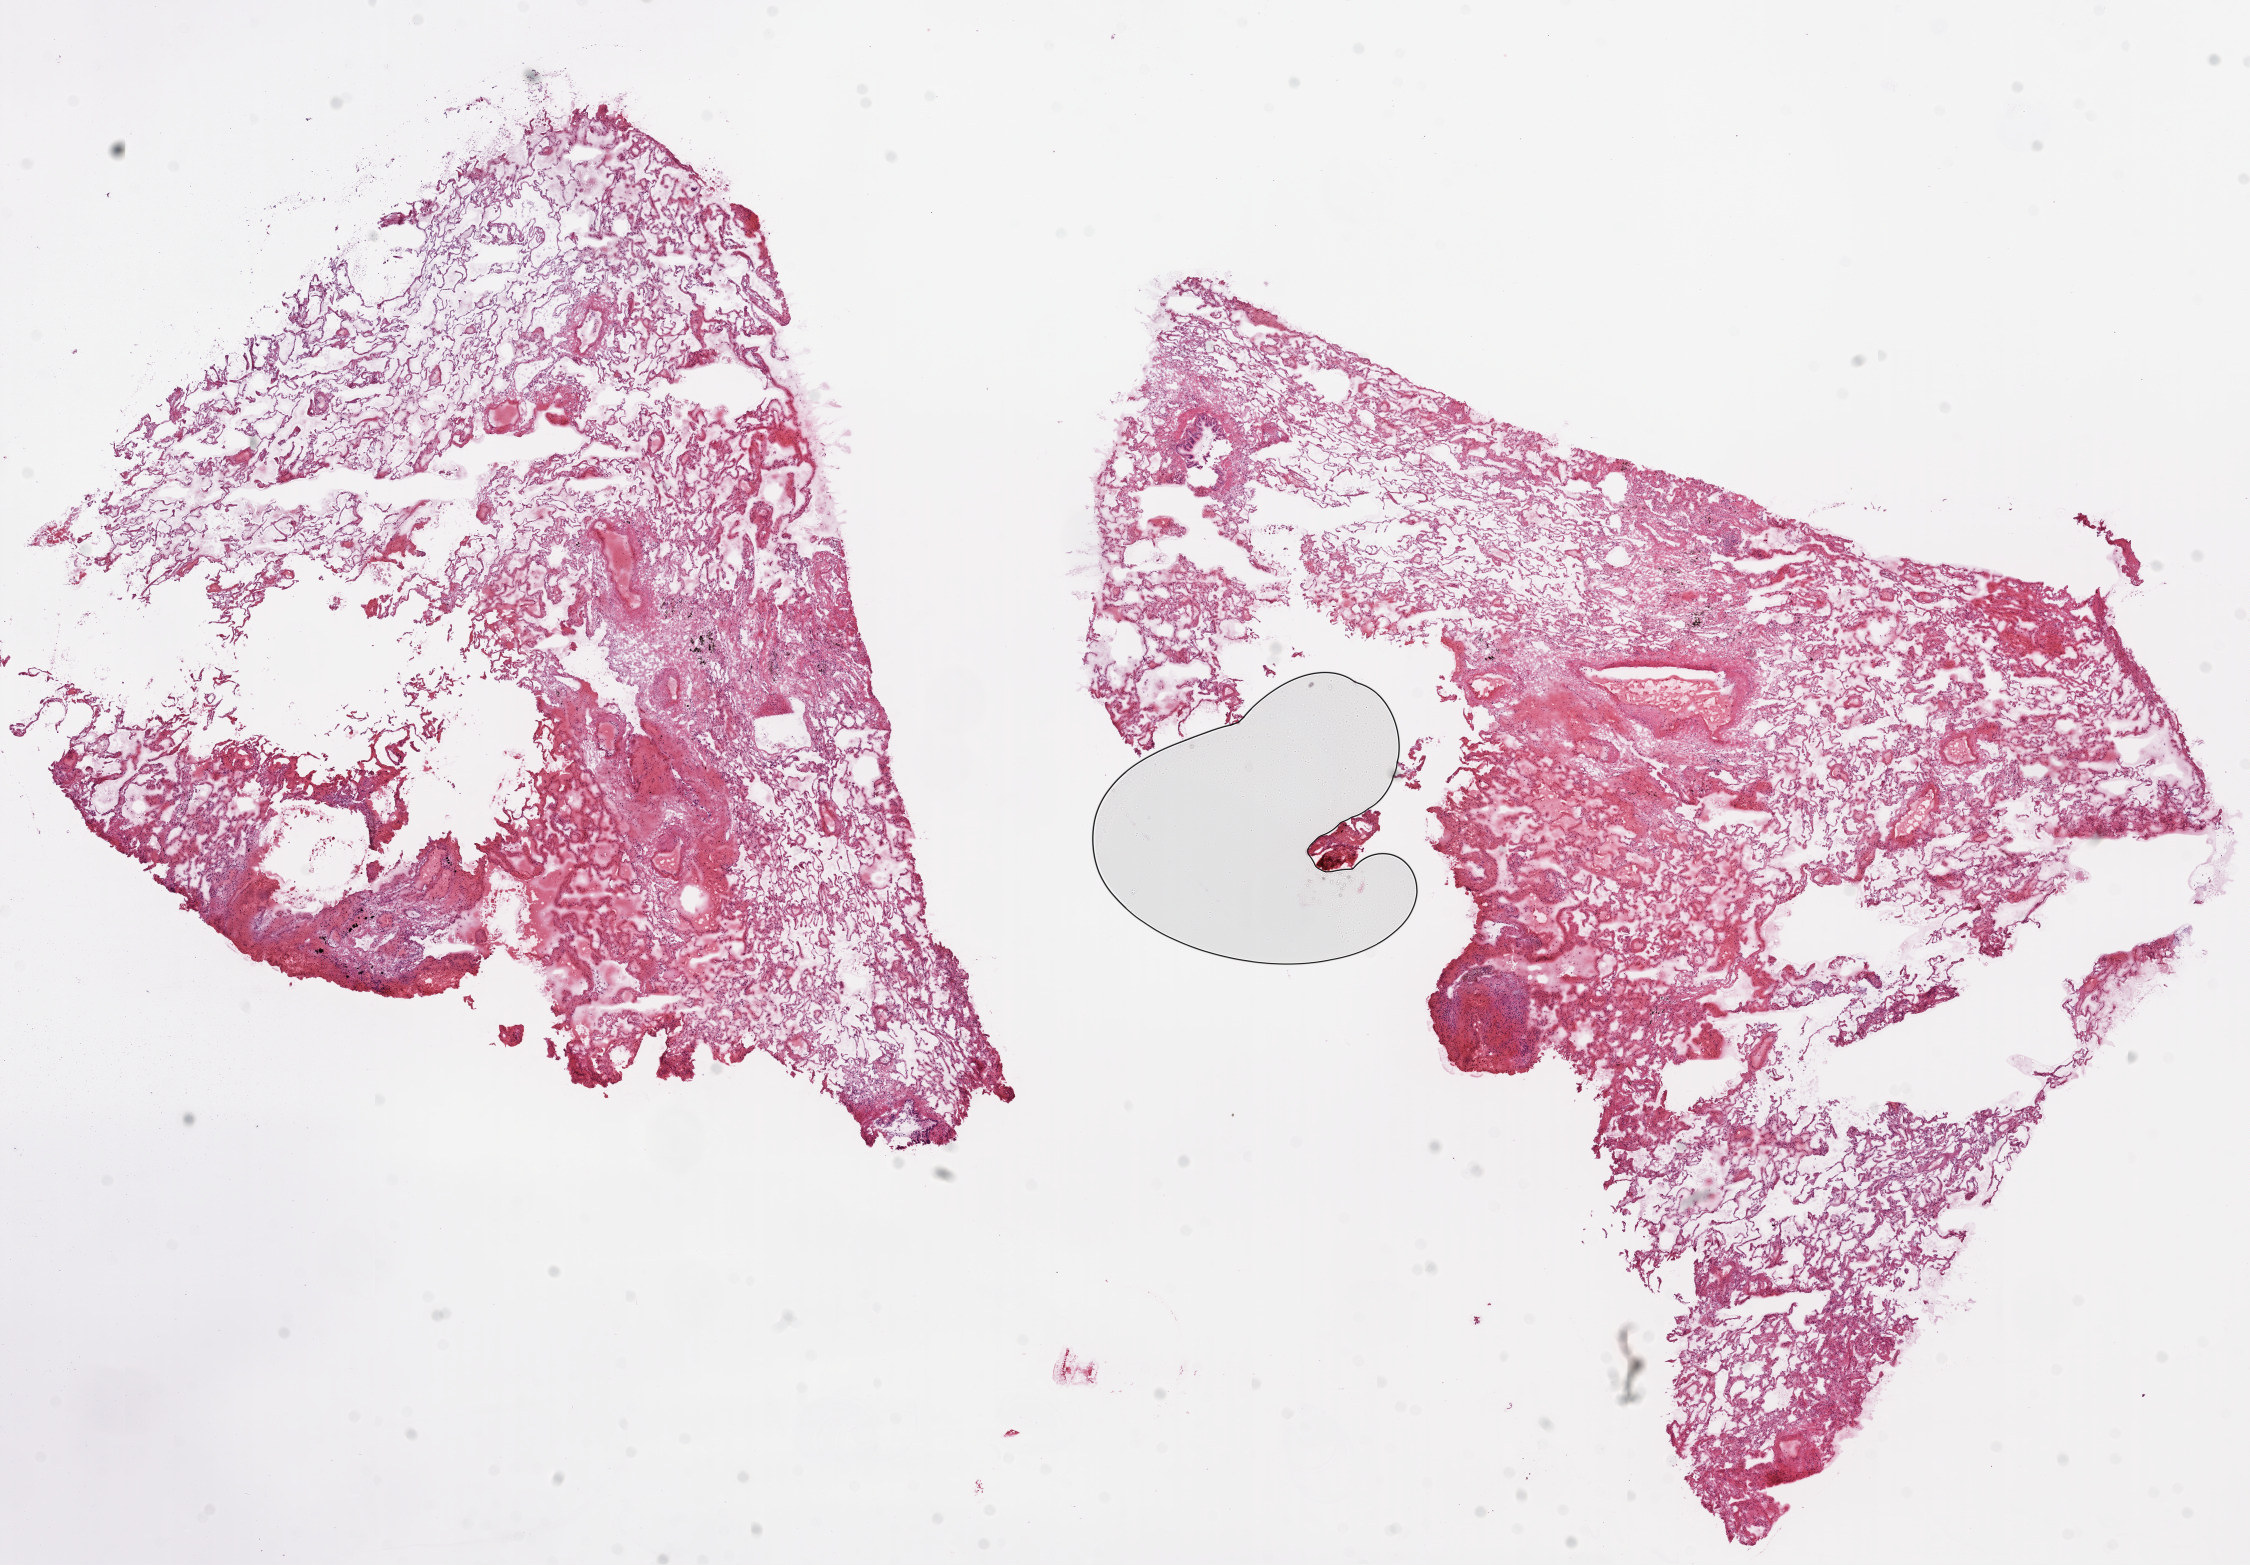
Whole-slide histology image, Hematoxylin and eosin (H&E) stained, low-resolution overview of the scanned area, about 18.1 x 12.6 mm; frozen section; solid tissue normal (non-tumour tissue) sample from the lung. Patient: male, age at initial diagnosis 66 years.
* this section: solid tissue normal (non-tumour) sample from the same patient
* patient diagnosis: Squamous cell carcinoma, NOS